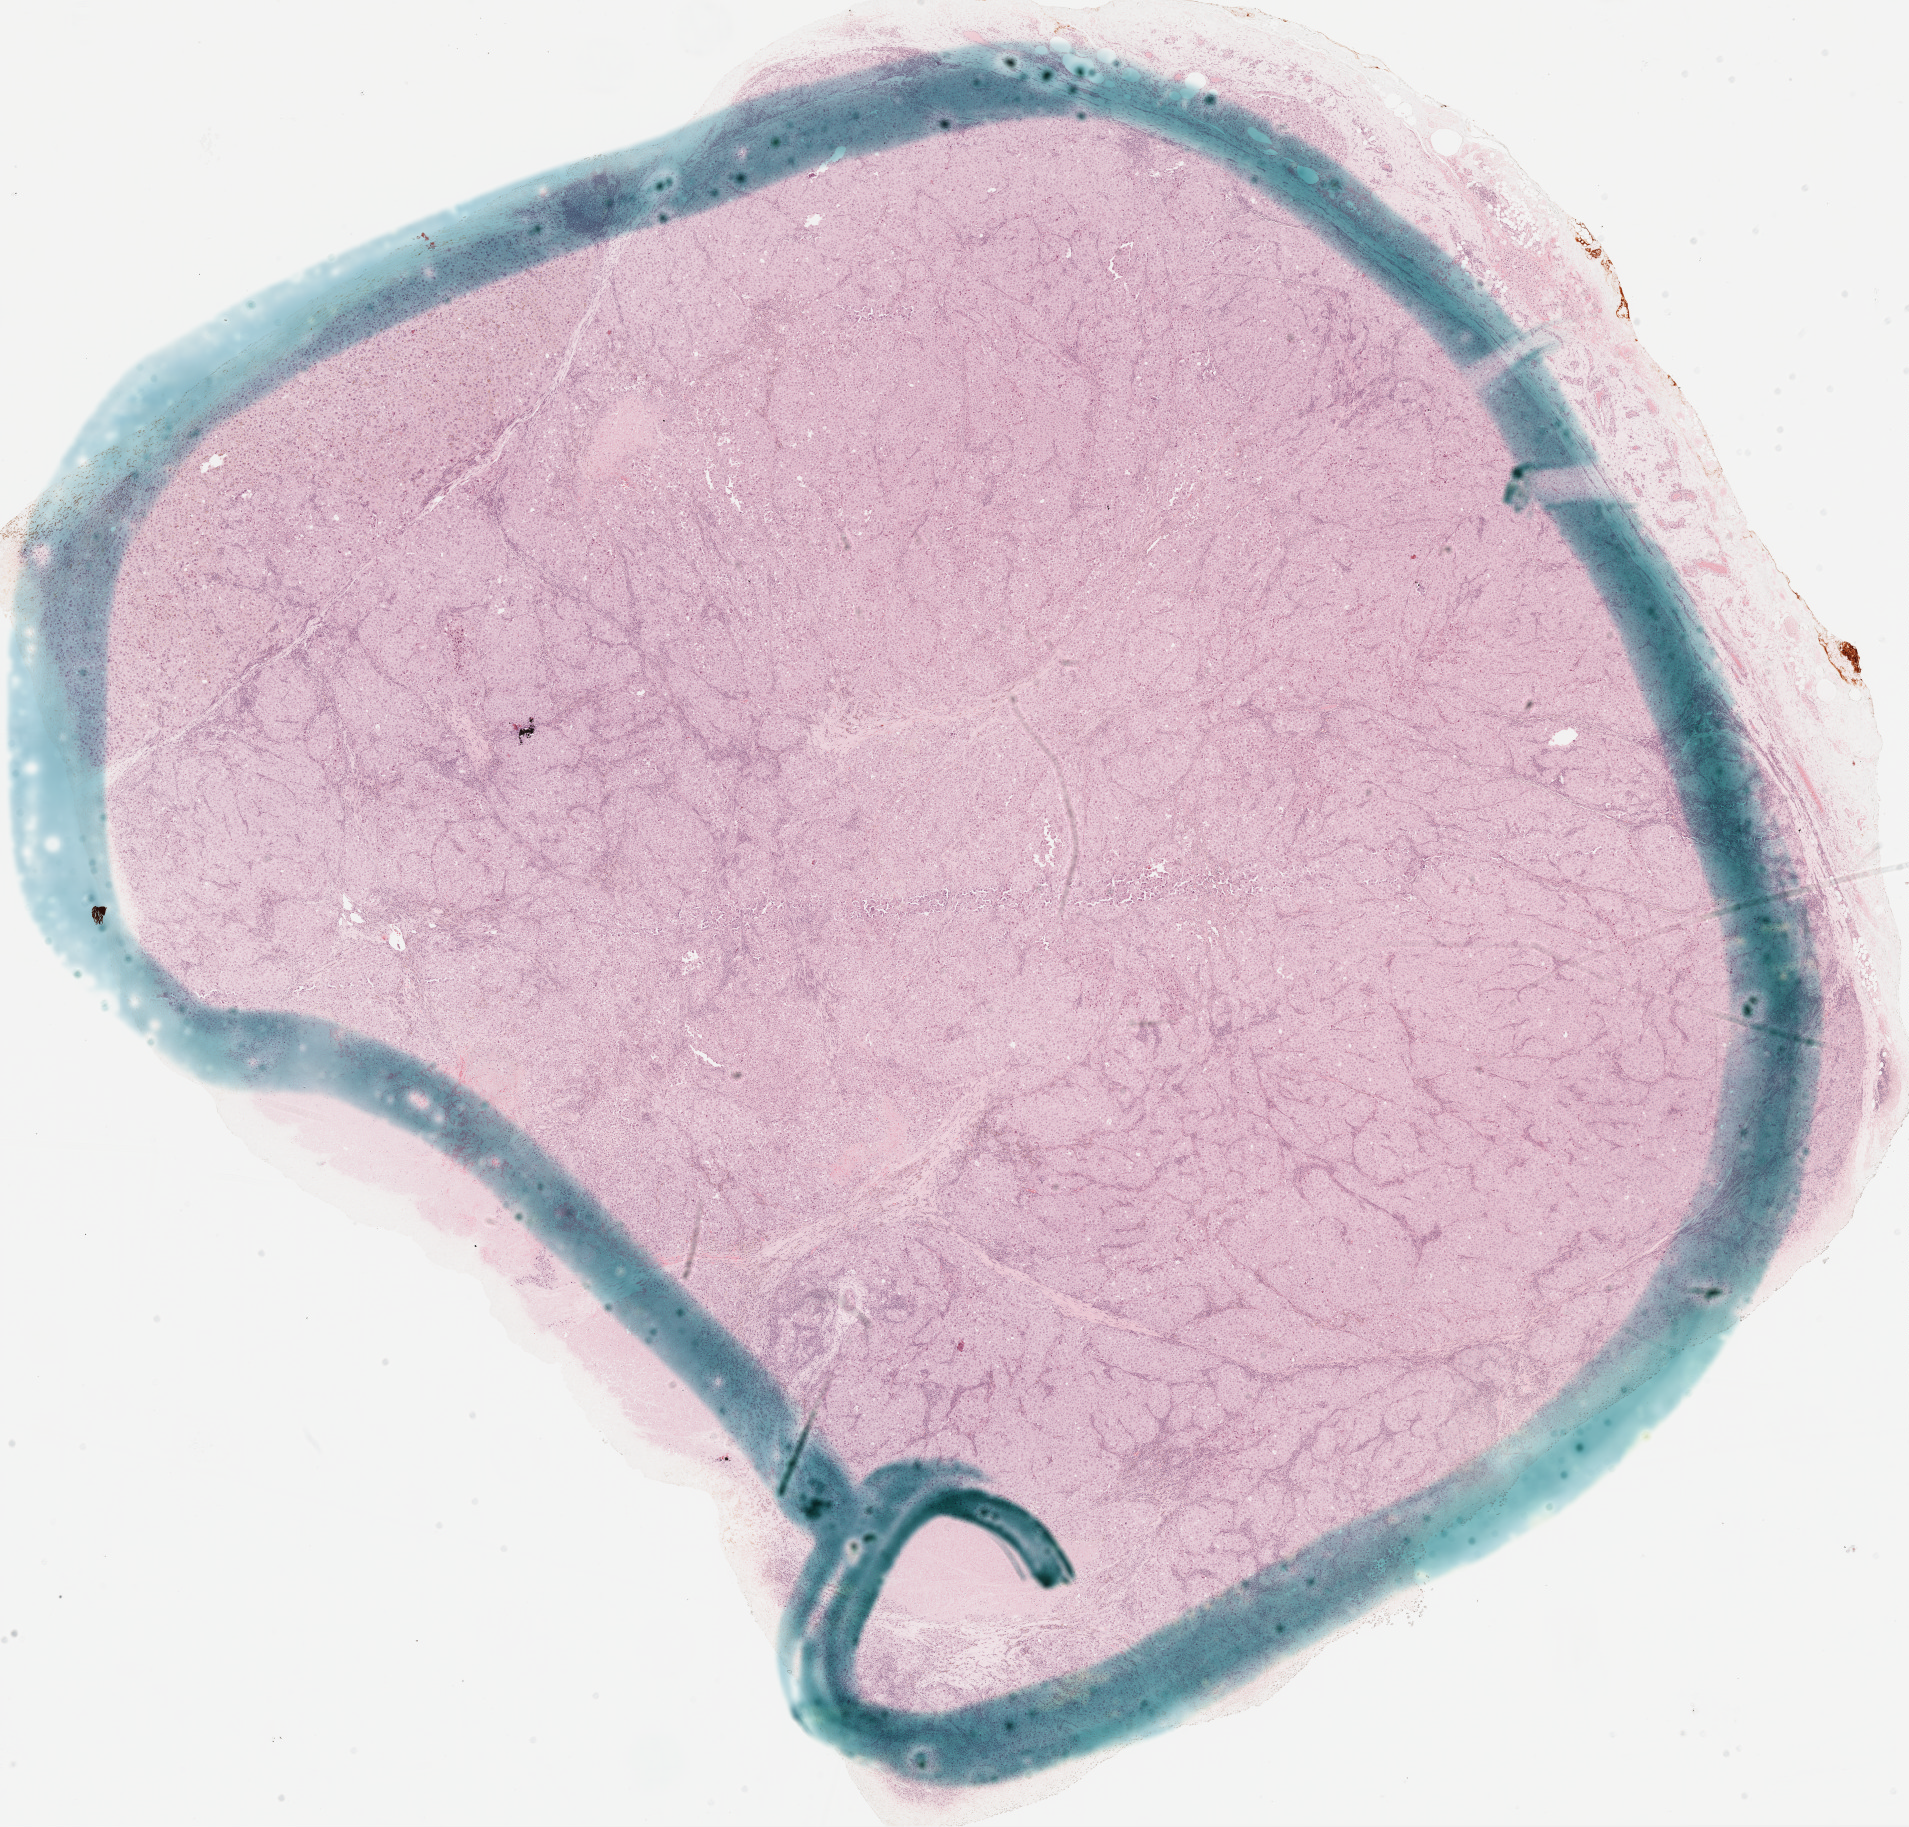
Digitized H&E tissue section (whole slide) — shown as a low-resolution overview of the whole scanned area (about 15.4 x 14.7 mm), formalin-fixed paraffin-embedded (FFPE) diagnostic section, metastatic tumour sample, sampled site not recorded. Male, age 67 years at initial diagnosis.
• this section: metastatic tumour tissue
• patient diagnosis: Malignant melanoma, NOS